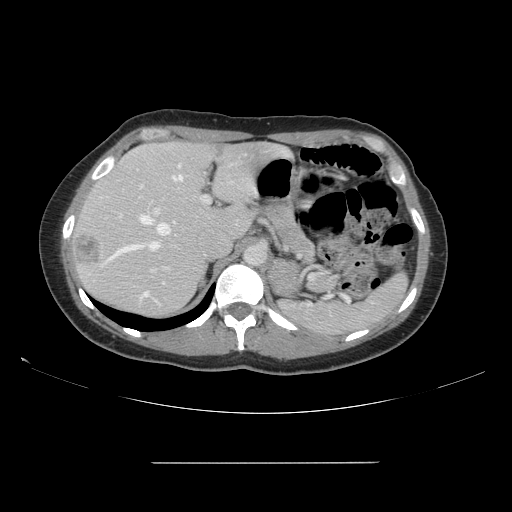
Contrast-enhanced abdominal CT, one axial slice; position 107 of 151 along the scan axis; 120 kVp; intravenous contrast given; soft-tissue window (W 400 / L 40 HU); 2.5 mm slice thickness; 512 × 512 image matrix. Female patient, age 46 years. From the clinical record (not read from this slice): diagnosis: colorectal cancer liver metastases, imaged before liver resection; multiple liver metastases: yes; largest metastasis: 3 cm; disease in both lobes: yes.
Annotated regions visible in this slice (manually delineated by an expert):
- hepatic veins: bounding box [x1, y1, x2, y2] px = [105, 165, 184, 263]
- liver: [72, 142, 282, 317]
- planned liver remnant (the part of the liver to remain after resection): [89, 142, 283, 253]
- portal vein (with intrahepatic branches): [139, 184, 210, 298]
- liver metastasis: [75, 236, 102, 266]
- liver metastasis: [212, 147, 224, 158]